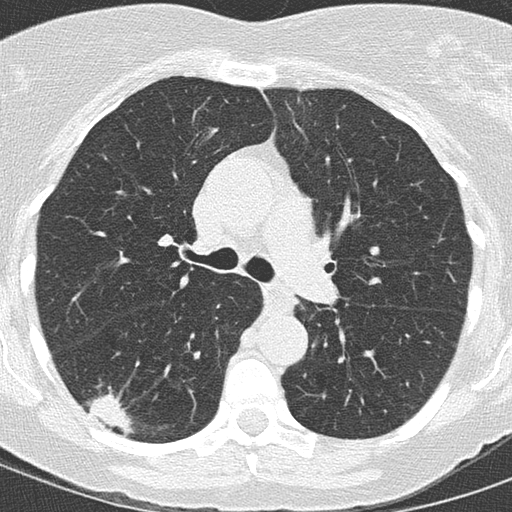
Axial slice from a low-dose chest CT screening exam, baseline annual screen, lung window (W 1500 / L -600 HU), 120 kVp, 512 × 512 image matrix, field of view 270 × 270 mm. Female, age 59 years at enrolment. Former smoker at enrolment.
• Expert reader's lesion annotation, bounding box <71,385,147,442> (left, top, right, bottom; pixels).
• The exam's reader record, not a measurement of the box and not confirmed to be the same lesion: non-calcified nodule or mass ≥4 mm, right lower lobe, 24 × 15 mm, spiculated (stellate) margins, soft tissue attenuation.
• Official screen result: positive, change unspecified: nodule(s) >= 4 mm or enlarging nodule(s), mass(es), or other non-specific abnormalities suspicious for lung cancer.
• Participant outcome: lung cancer diagnosed 12 days after this screen — adenocarcinoma, NOS, right lower lobe, moderately differentiated (G2), stage IIB (AJCC 6th edition), 22 mm at pathology.